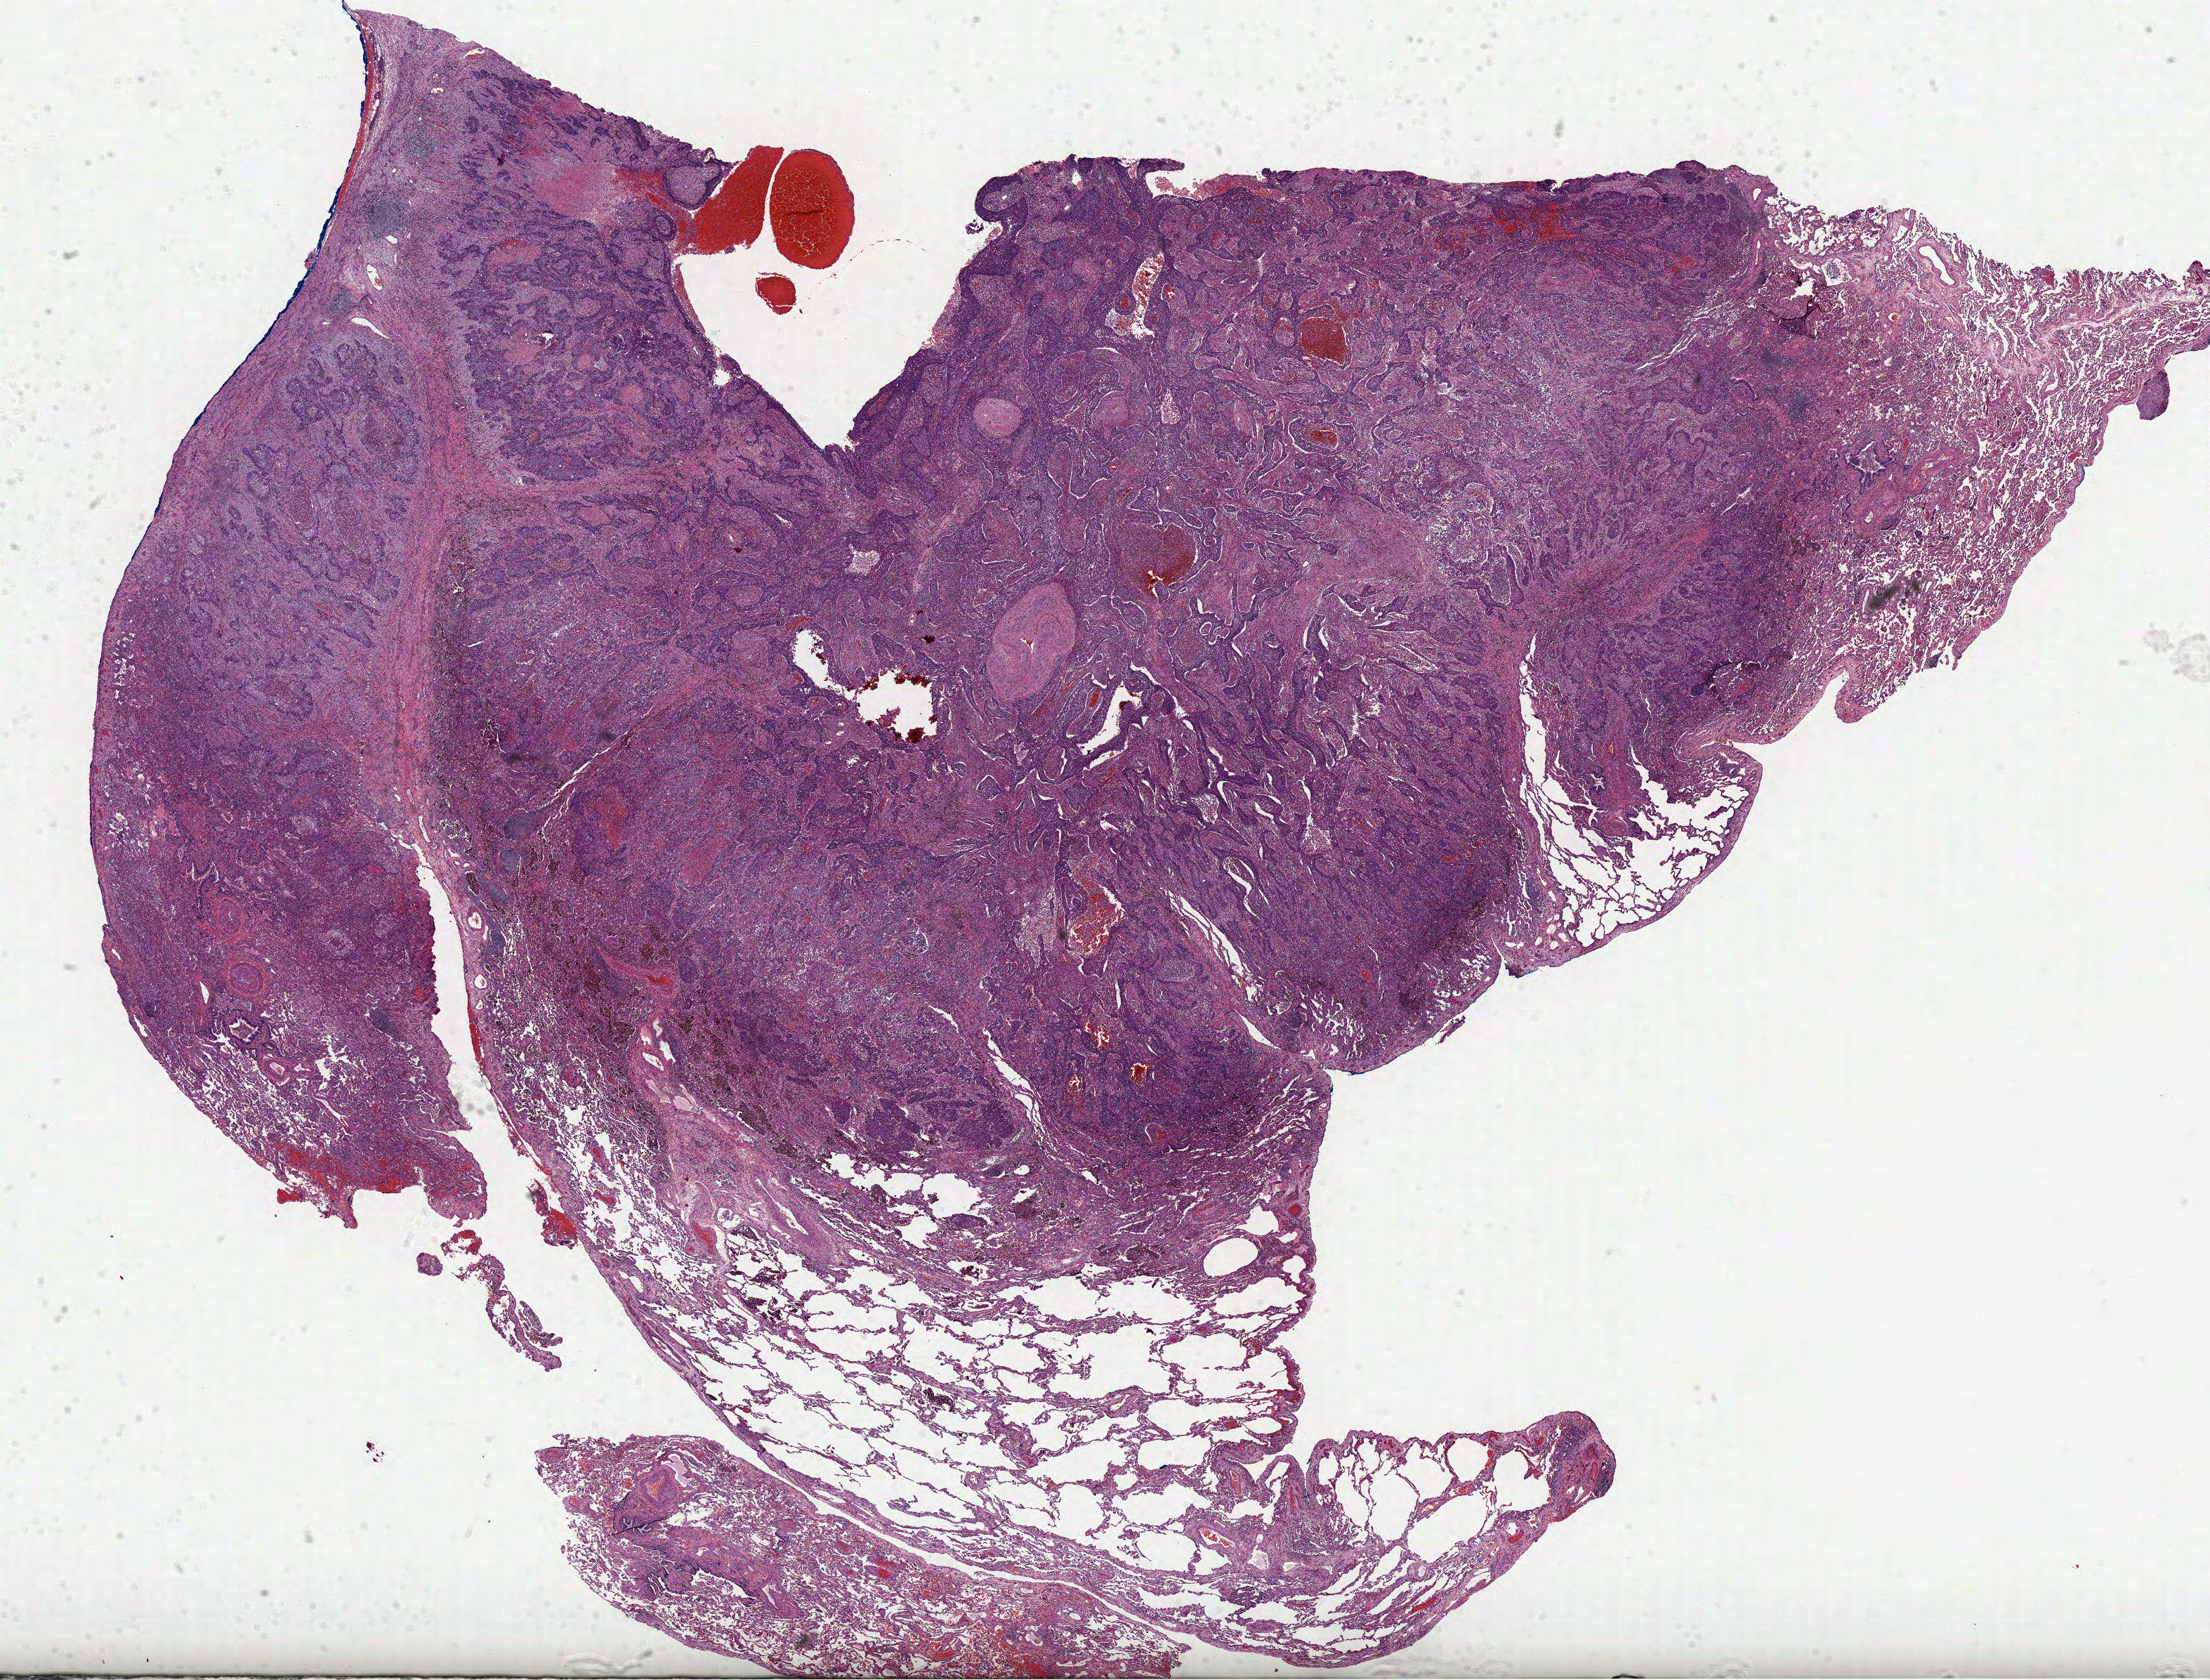
Digitized Hematoxylin and eosin (H&E) stained tissue section (whole slide), whole scanned area (about 25.4 x 19.3 mm, slide scanned at 40x) shown as a low-resolution overview, formalin-fixed paraffin-embedded (FFPE) diagnostic section, lung, primary tumour sample. Patient: female, age at initial diagnosis 83 years.
* TNM: T2 N1 M0
* AJCC pathologic stage: IIB (7th edition)
* pathologic diagnosis: Squamous cell carcinoma, NOS (lower lobe, lung)
* laterality: left